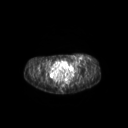
FDG PET of an extremity soft-tissue mass (from a PET/CT study), one axial slice. Position 76 of 267 along the scan axis. 128 × 128 image matrix, field of view 600 × 600 mm. Female patient, age 24 years. Case-level facts recorded for this patient, not image findings: histological type: leiomyosarcoma; grade: high; site of the primary tumour: groin.
Annotated regions visible in this slice (expert contour drawn on MRI and transferred to this co-registered scan by the dataset authors):
- gross tumour volume including surrounding oedema: bounding box [x1, y1, x2, y2] px = [70, 54, 94, 64]
- gross tumour volume (mass): [72, 55, 83, 64]